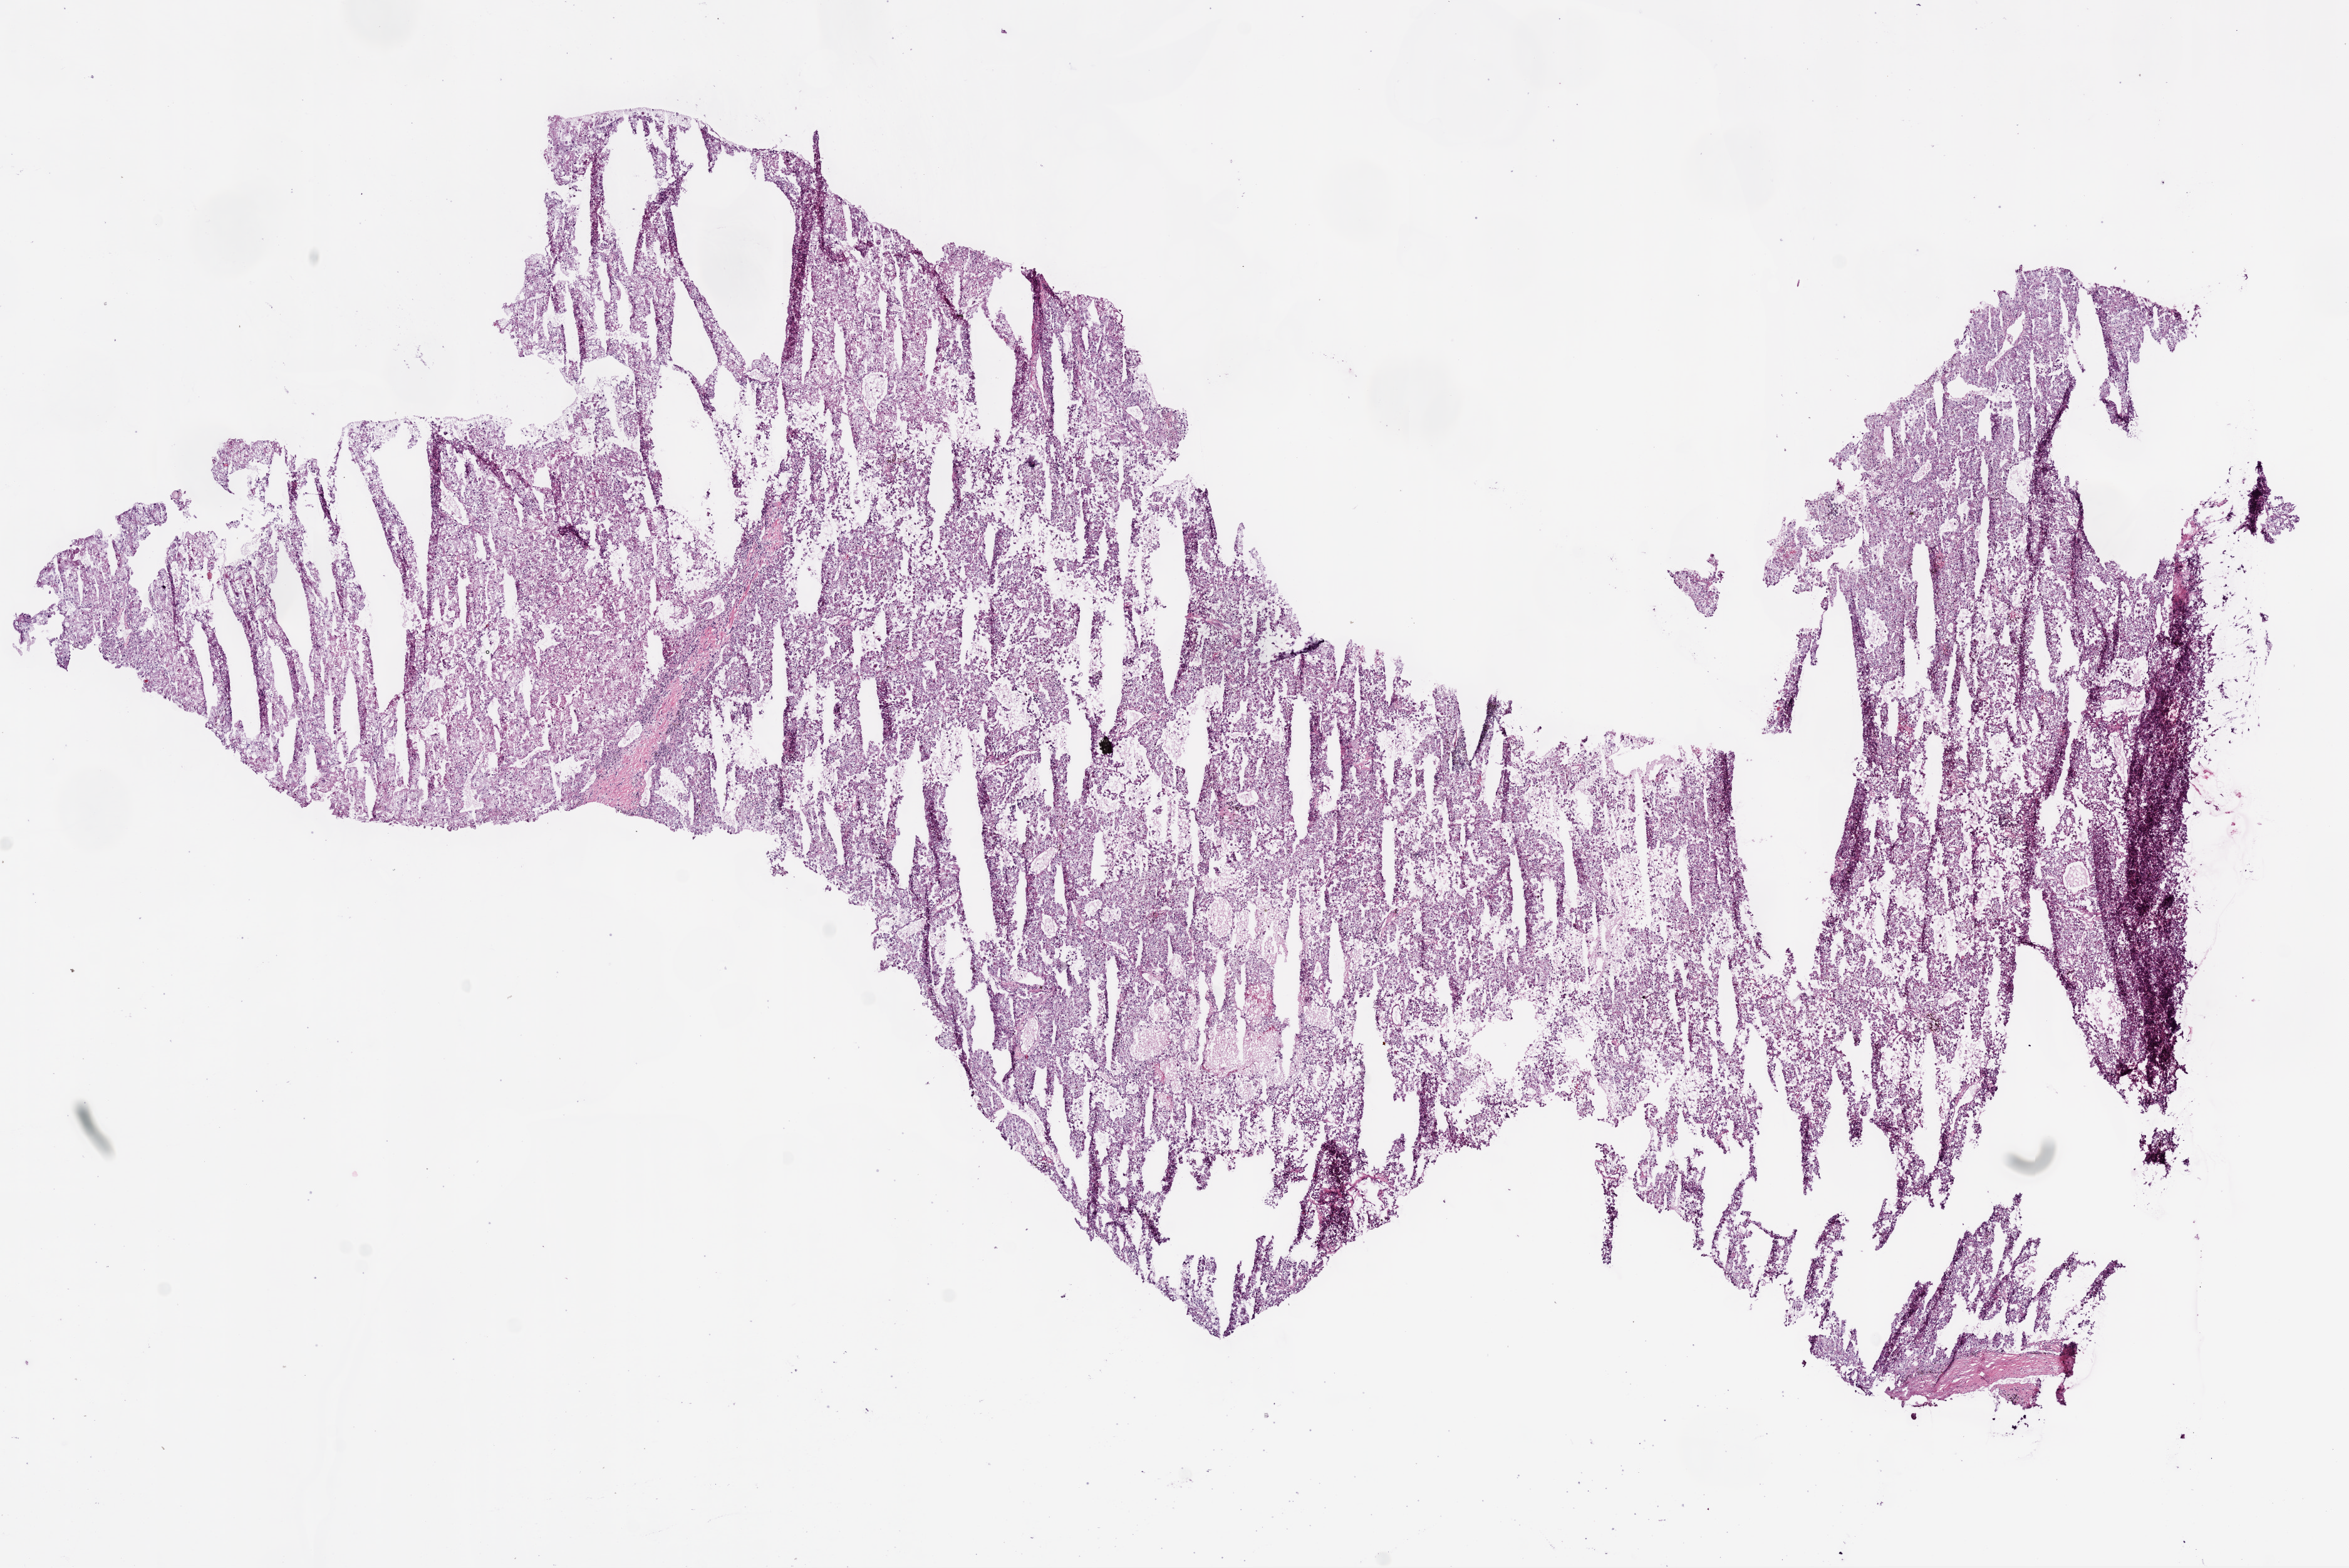
Whole-slide histology image, H&E, a low-resolution overview of the entire scanned area, about 15.0 x 10.0 mm (acquisition: 20x scan), frozen section from the bottom of the tissue portion, kidney, primary tumour sample. Male patient; age at initial diagnosis 43 years. Histologic grade: G3 (poorly differentiated). Pathologist review of this section (percent, as recorded): tumour cells 90%, tumour nuclei 80%, normal cells 0%, stromal cells 10%, necrosis 0%.
• AJCC pathologic stage: I
• histologic diagnosis: Clear cell adenocarcinoma, NOS